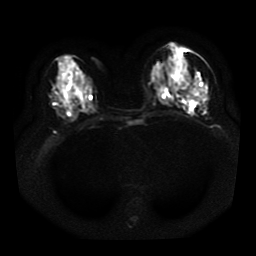
Breast MRI, one axial slice. Position 17 of 41 along the scan axis. Diffusion-weighted series; image 2 of 4 stored at this slice position (different b-values; order by instance number). 1.5 T. 5 mm slice thickness. 256 × 256 image matrix, field of view 330 × 330 mm. Female patient.
Annotated regions visible in this slice (expert manual segmentation):
- tumour on diffusion-weighted imaging: box from (x=173, y=85) to (x=178, y=91) px